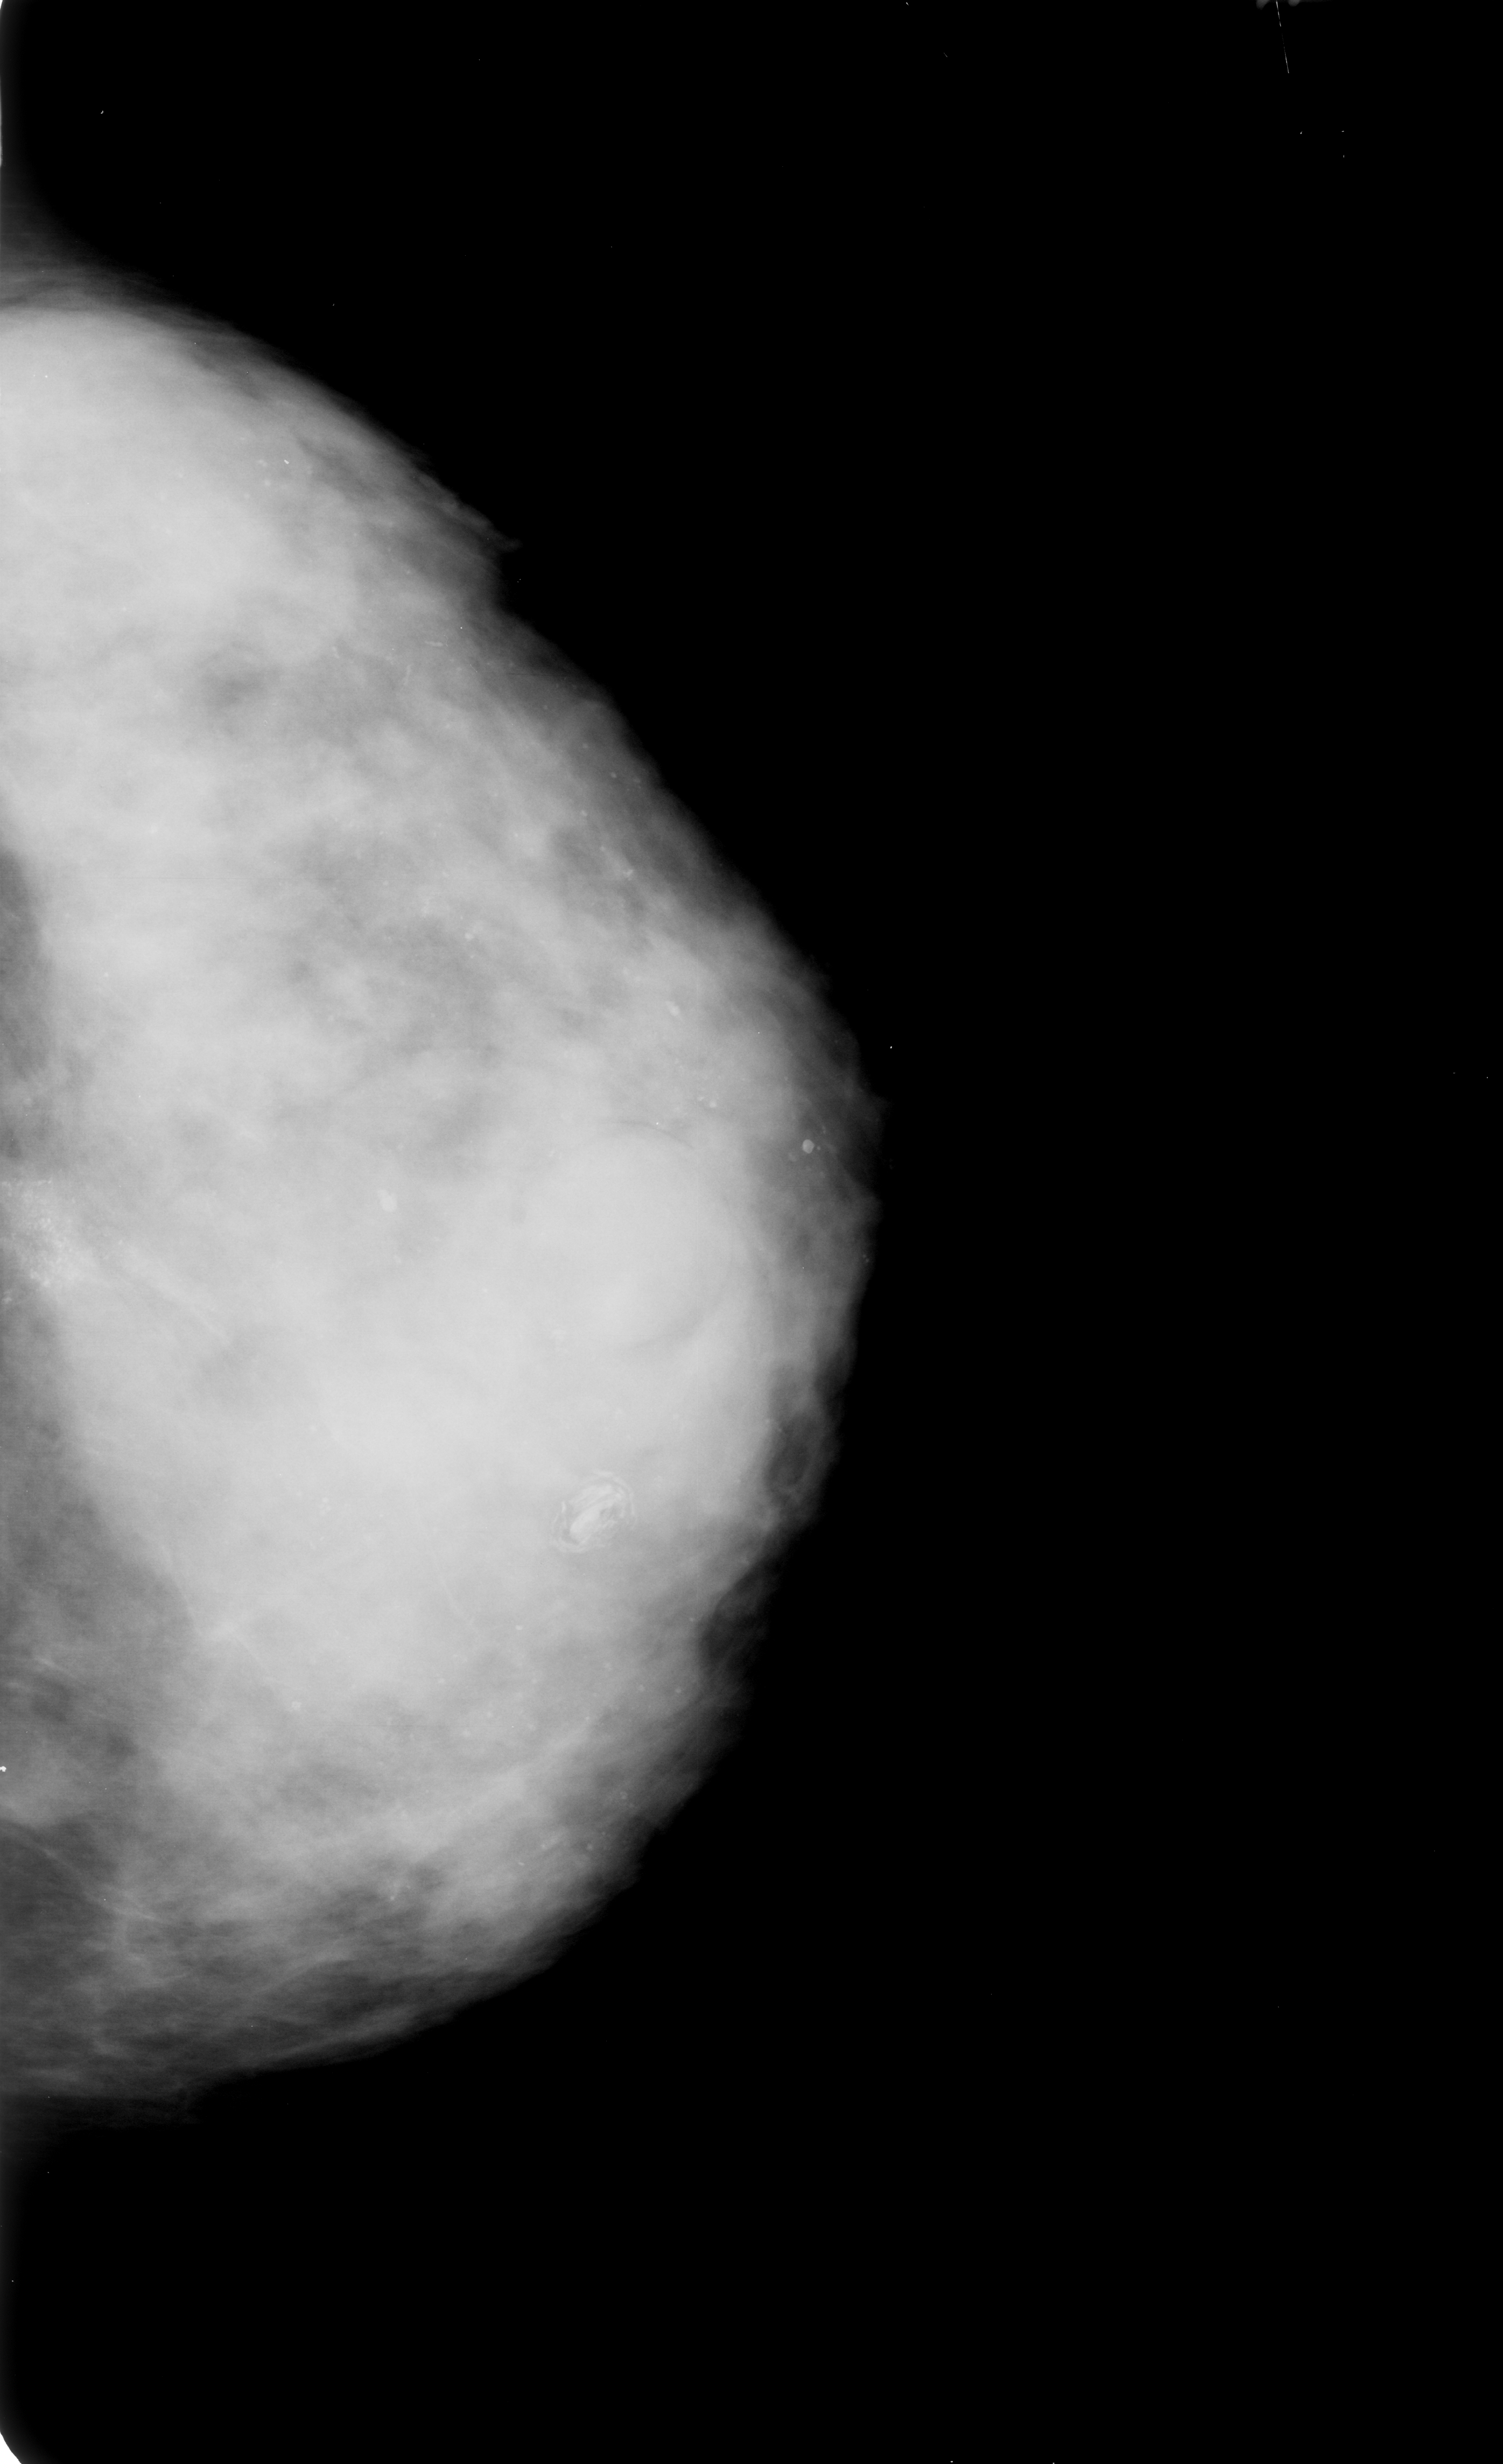
Scanned film-screen mammogram, left breast, craniocaudal (CC) view, BI-RADS breast density category 4 (scale 1–4).
- Marked findings (only marked abnormalities are described; nothing is implied about the rest of the image): calcifications, morphology pleomorphic, distribution clustered; BI-RADS assessment category 4; subtlety rating 3 on a 1 (subtle) to 5 (obvious) scale; pathology (as recorded): malignant.